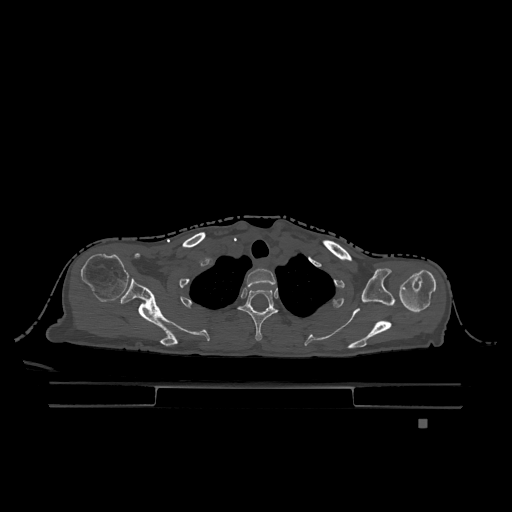
CT including the spine, one axial slice; position 965 of 1317 along the scan axis; bone window (W 1800 / L 400 HU); 0.5 mm slice thickness; 512 × 512 image matrix. Patient: female, 74 years. Case-level facts recorded for this patient, not image findings: primary cancer: lung; vertebrae with lytic lesions (as recorded): T1, T4, T5, T6, L4, L5.
Annotated regions visible in this slice (semi-automatically segmented with operator editing):
- T1 vertebra: bounding box [x1, y1, x2, y2] px = [246, 268, 276, 288]
- T2 vertebra: [238, 289, 278, 341]